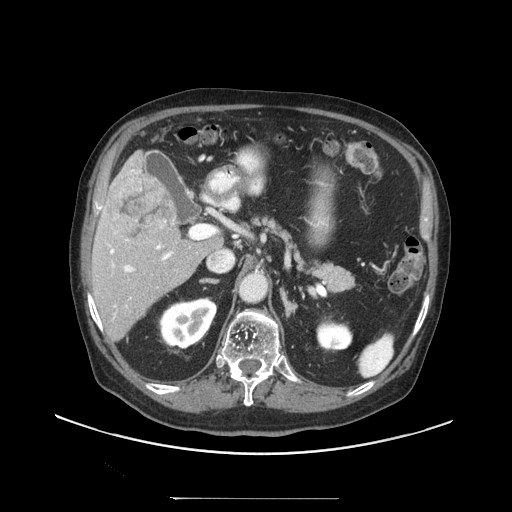
Contrast-enhanced abdominal CT (liver protocol), one axial slice. Position 57 of 97 along the scan axis. 140 kVp. Soft-tissue window (W 400 / L 40 HU). 512 × 512 image matrix, field of view 450 × 450 mm. From the clinical record (not read from this slice): diagnosis: hepatocellular carcinoma (patient treated with transarterial chemoembolisation; whether this scan precedes or follows treatment is not stated here); TNM stage (as recorded): Stage-IIIC; Child-Pugh class: A; tumour differentiation: well differentiated; tumour nodularity: uninodular.
Structures marked on this image (semi-automatically segmented with operator editing):
- liver parenchyma outside the tumour (the mass and vessels are separate outlines, so this box may not span the whole liver): bounding box (x1, y1, x2, y2) in pixels: (90, 150, 208, 340)
- mass: (106, 175, 175, 242)
- liver vessels: (110, 169, 173, 272)